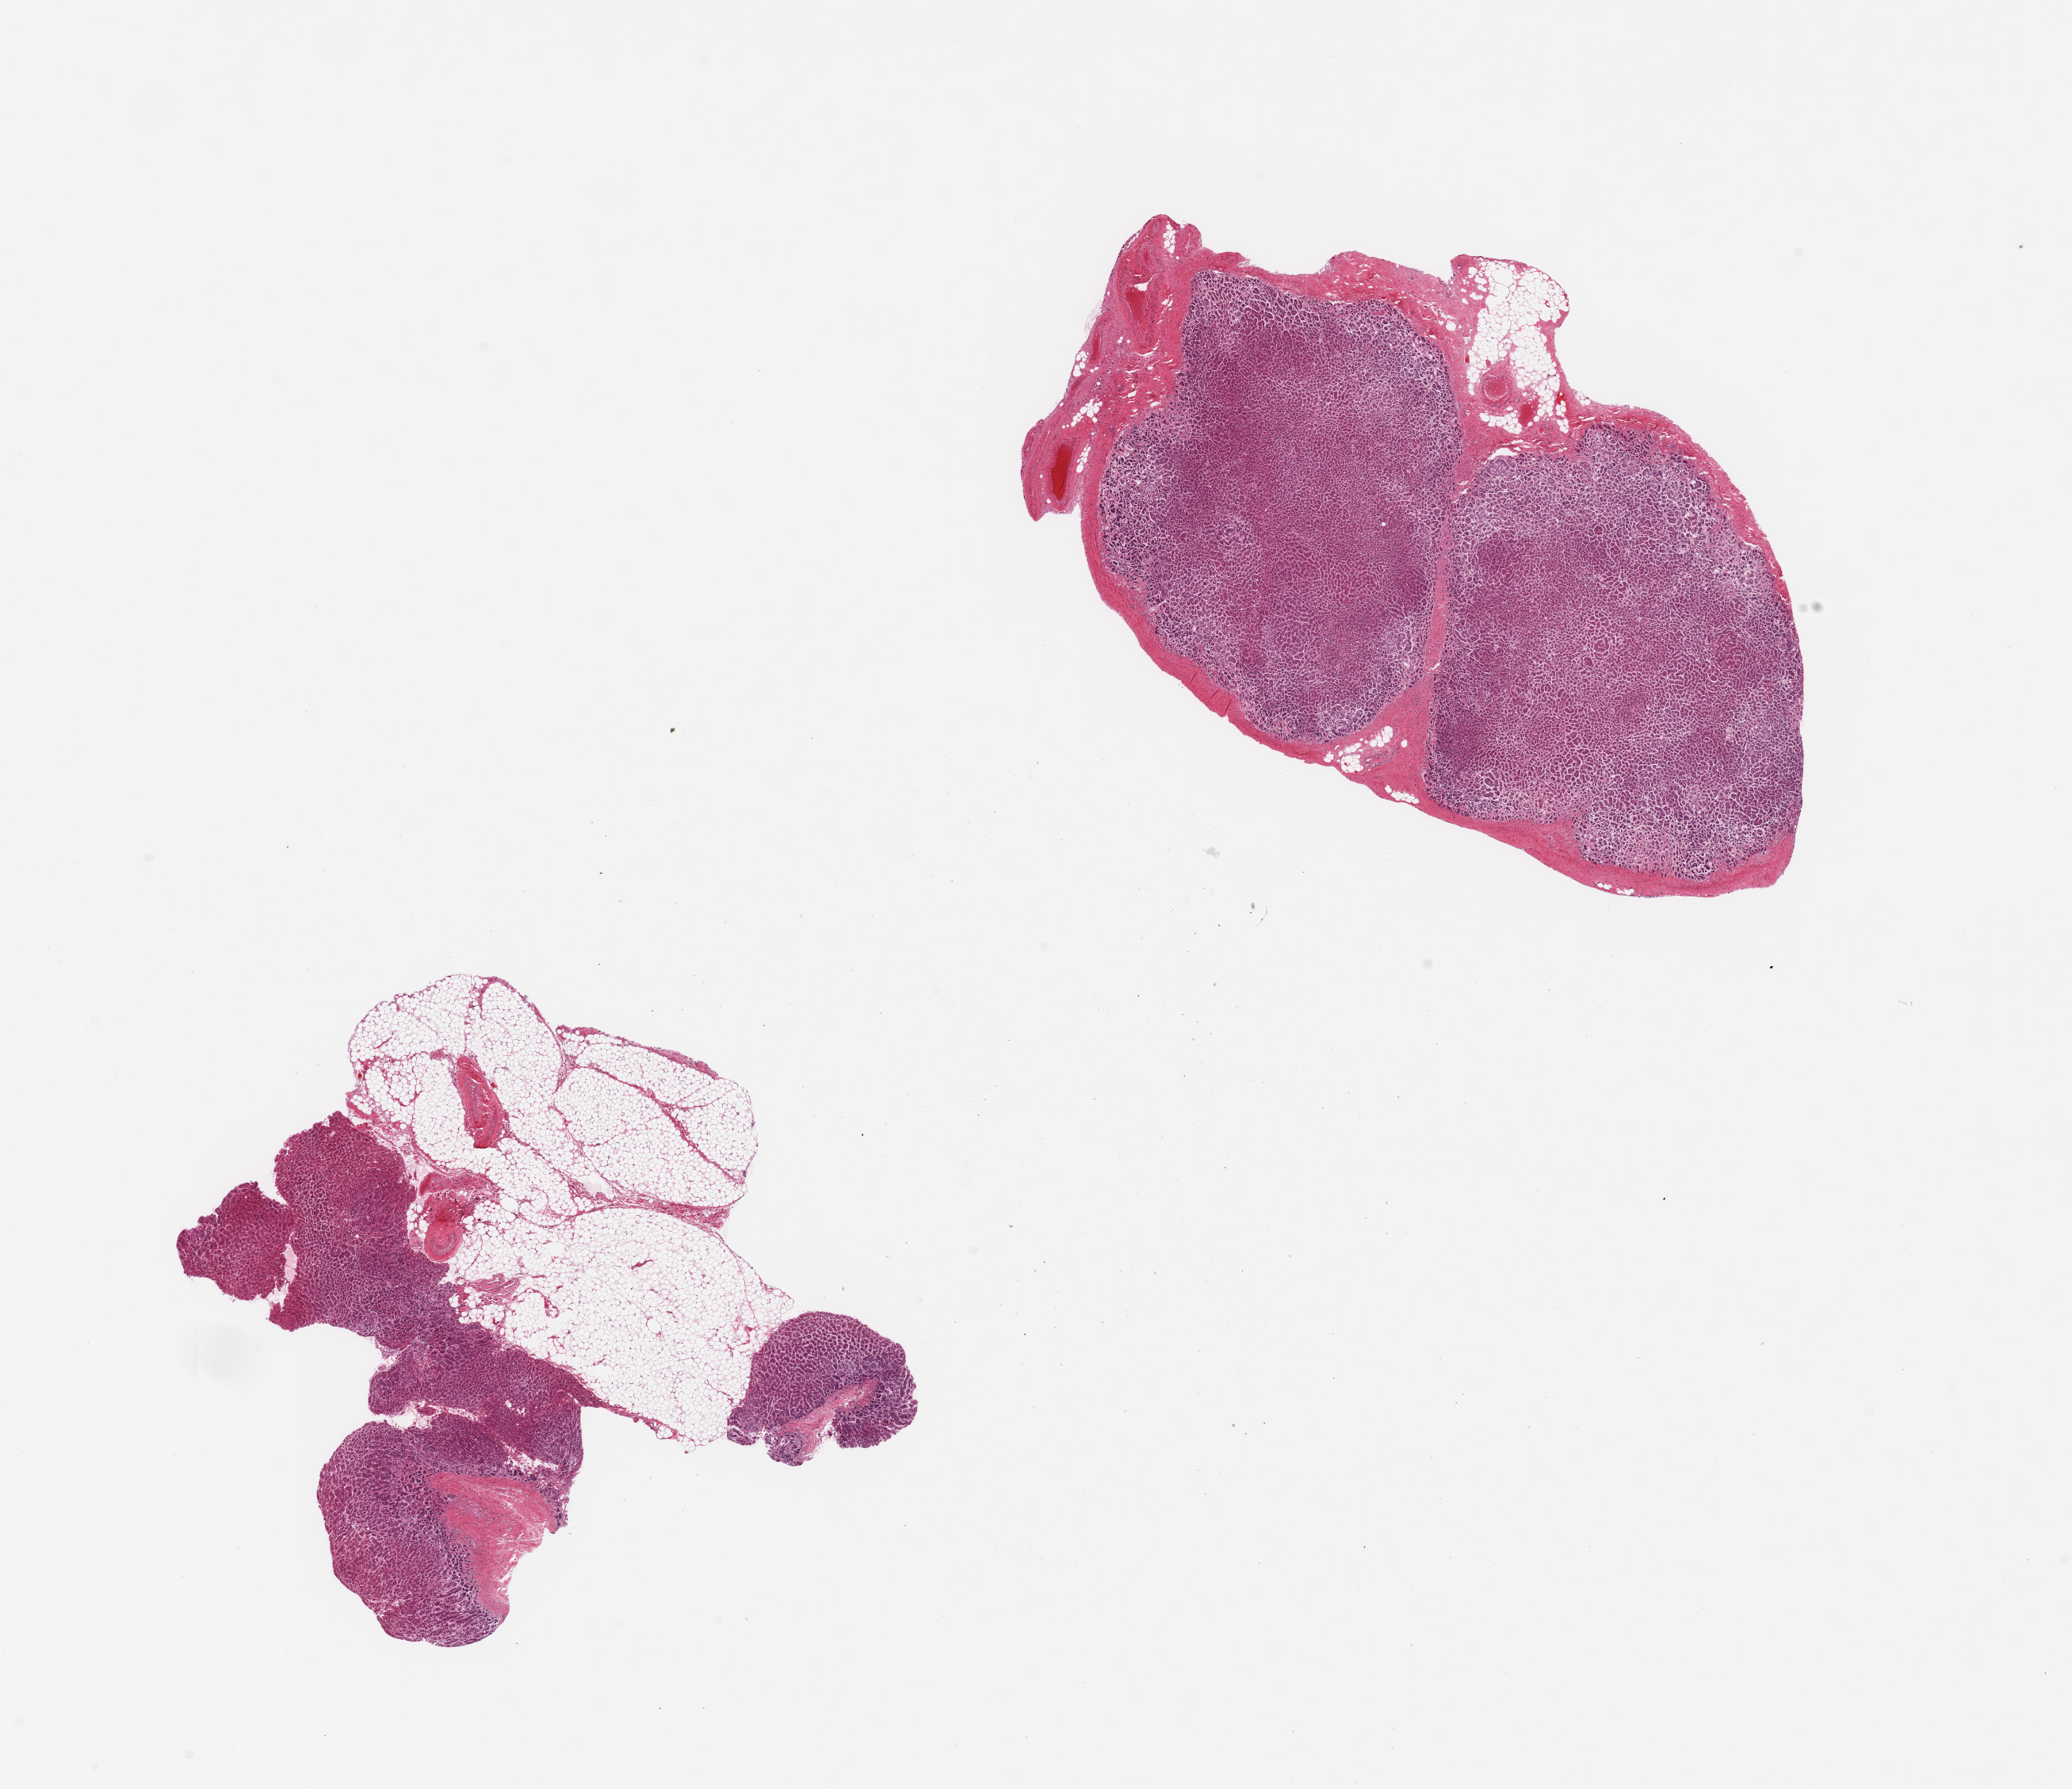
Whole-slide image, haematoxylin and eosin stain, a low-resolution overview of the entire scanned area, about 20.7 x 17.8 mm, PAXgene-fixed paraffin-embedded (PFPE) section, section of adrenal gland (target tissue), tissue donor sample.
- reviewer comment on this tissue sample: 2 pieces; 1 with 50% fat, other with 5% fat